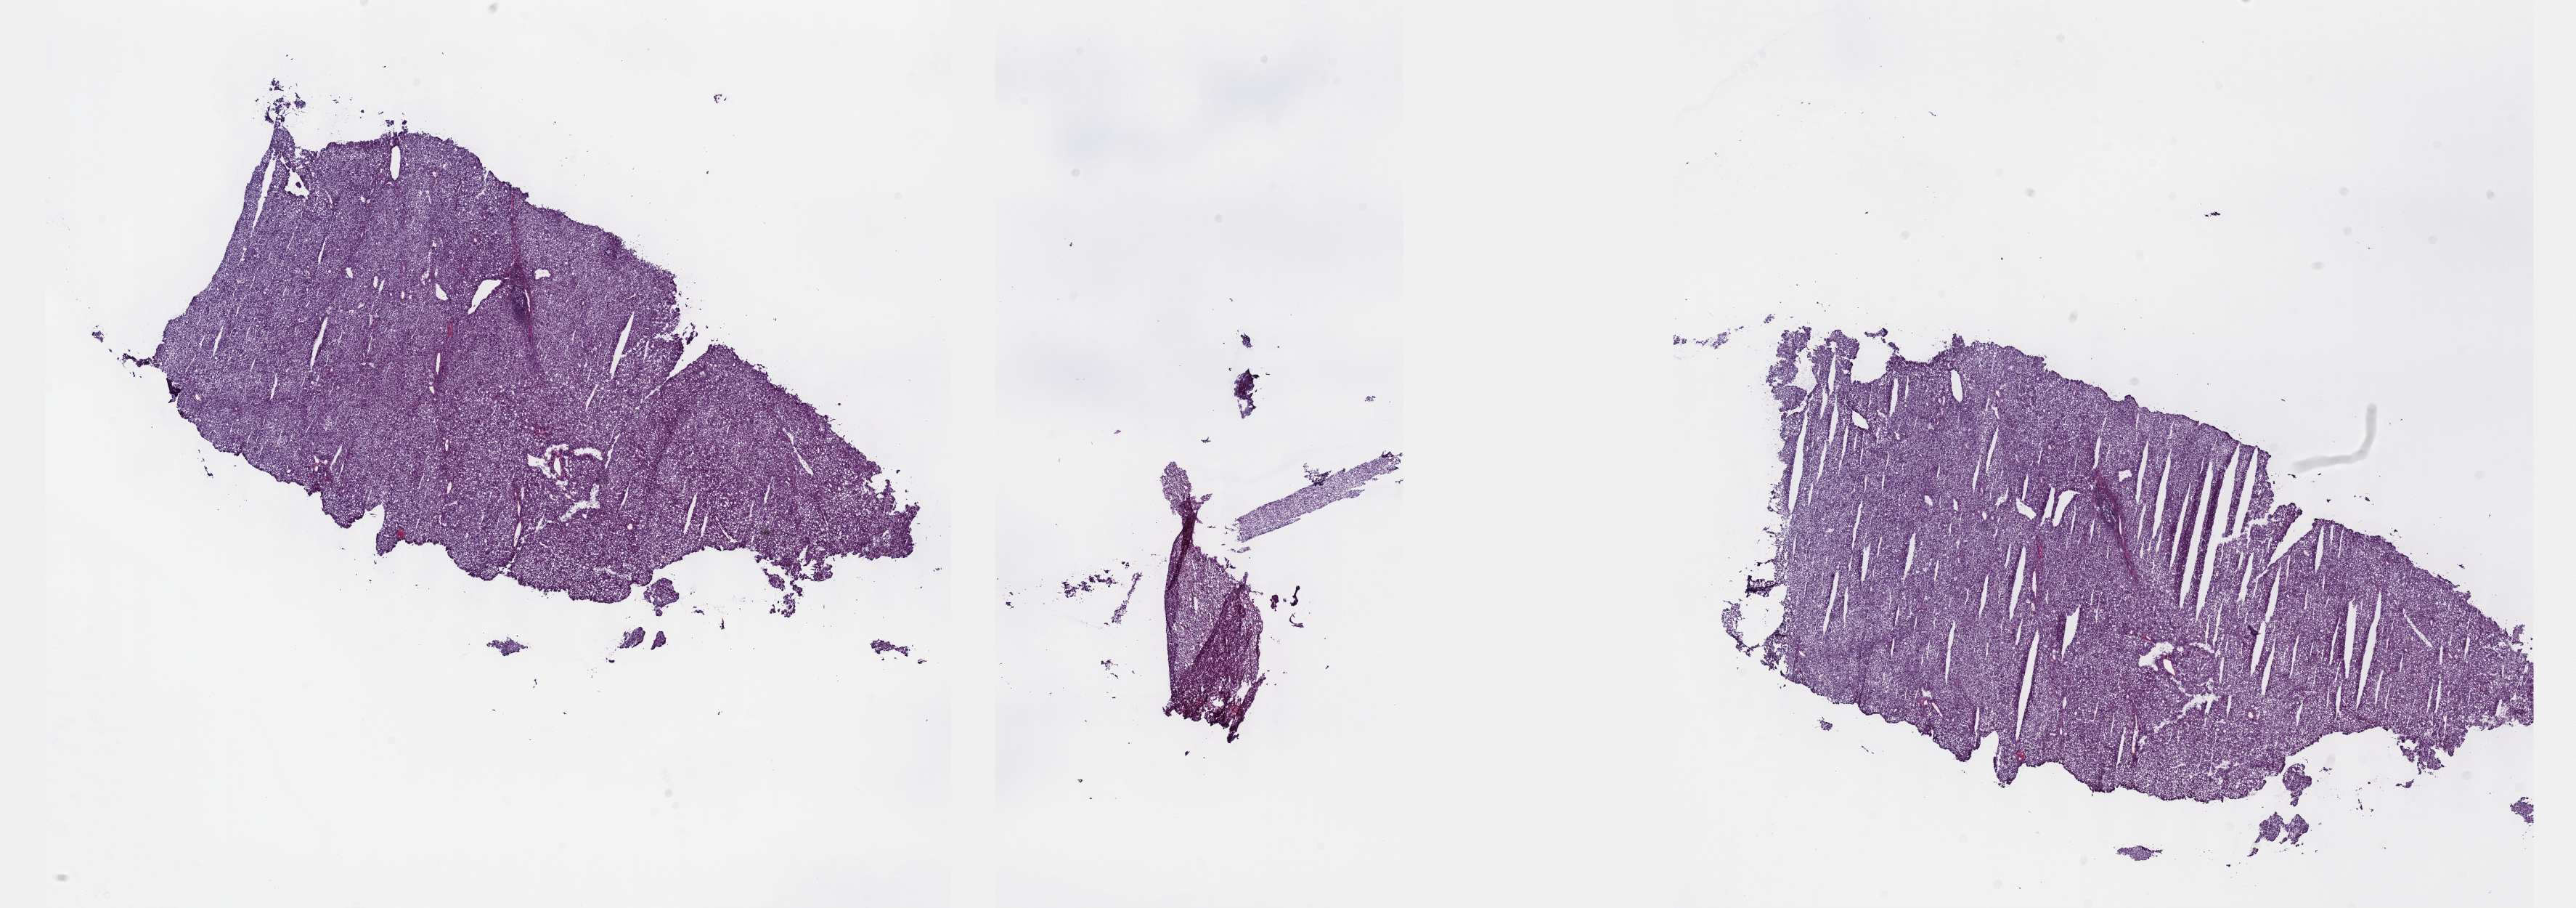
Digitized H&E tissue section (whole slide) — low-resolution overview of the scanned area, about 28.7 x 10.1 mm (slide scanned at 40x), frozen section from the top of the tissue portion, primary tumour sample from the liver. Patient: male, age at initial diagnosis 58 years. Histologic grade: G2 (moderately differentiated). Pathologist review of this section (percent, as recorded): tumour cells 85%, tumour nuclei 85%, normal cells 0%, stromal cells 15%, necrosis 0%. Inflammatory infiltration, as recorded: lymphocyte infiltration 3%, monocyte infiltration 1%, neutrophil infiltration 2%.
Histologic diagnosis: Hepatocellular carcinoma, NOS. AJCC pathologic stage: I (7th edition).